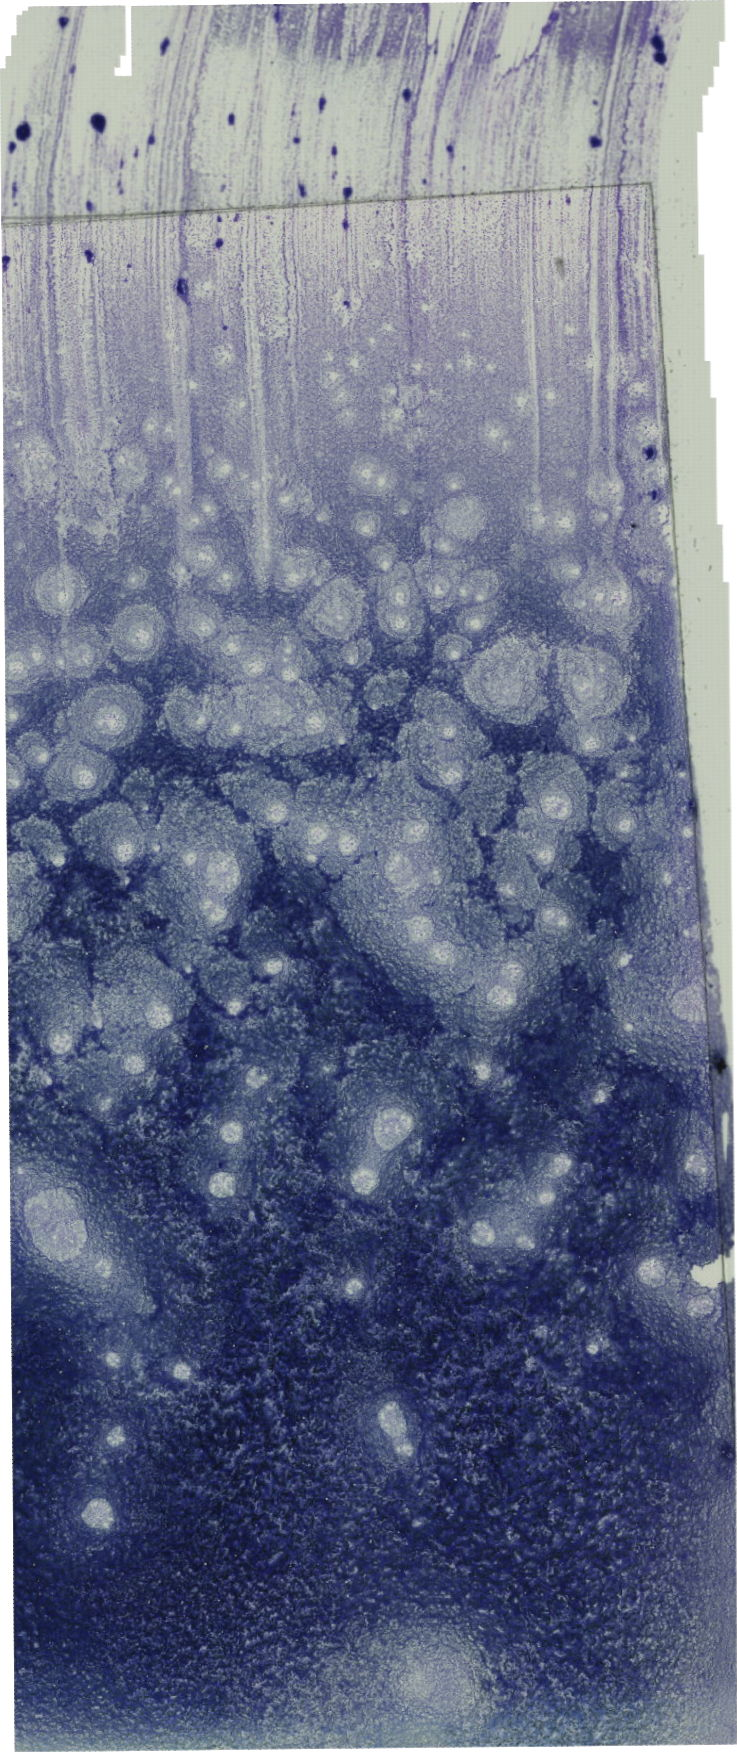
Bone marrow aspirate smear, May-Grünwald–Giemsa stain, whole-slide image, a low-resolution overview of the entire scanned area, about 20.9 x 49.7 mm. Male patient.
Diagnosis: T Acute Lymphoblastic Leukemia.